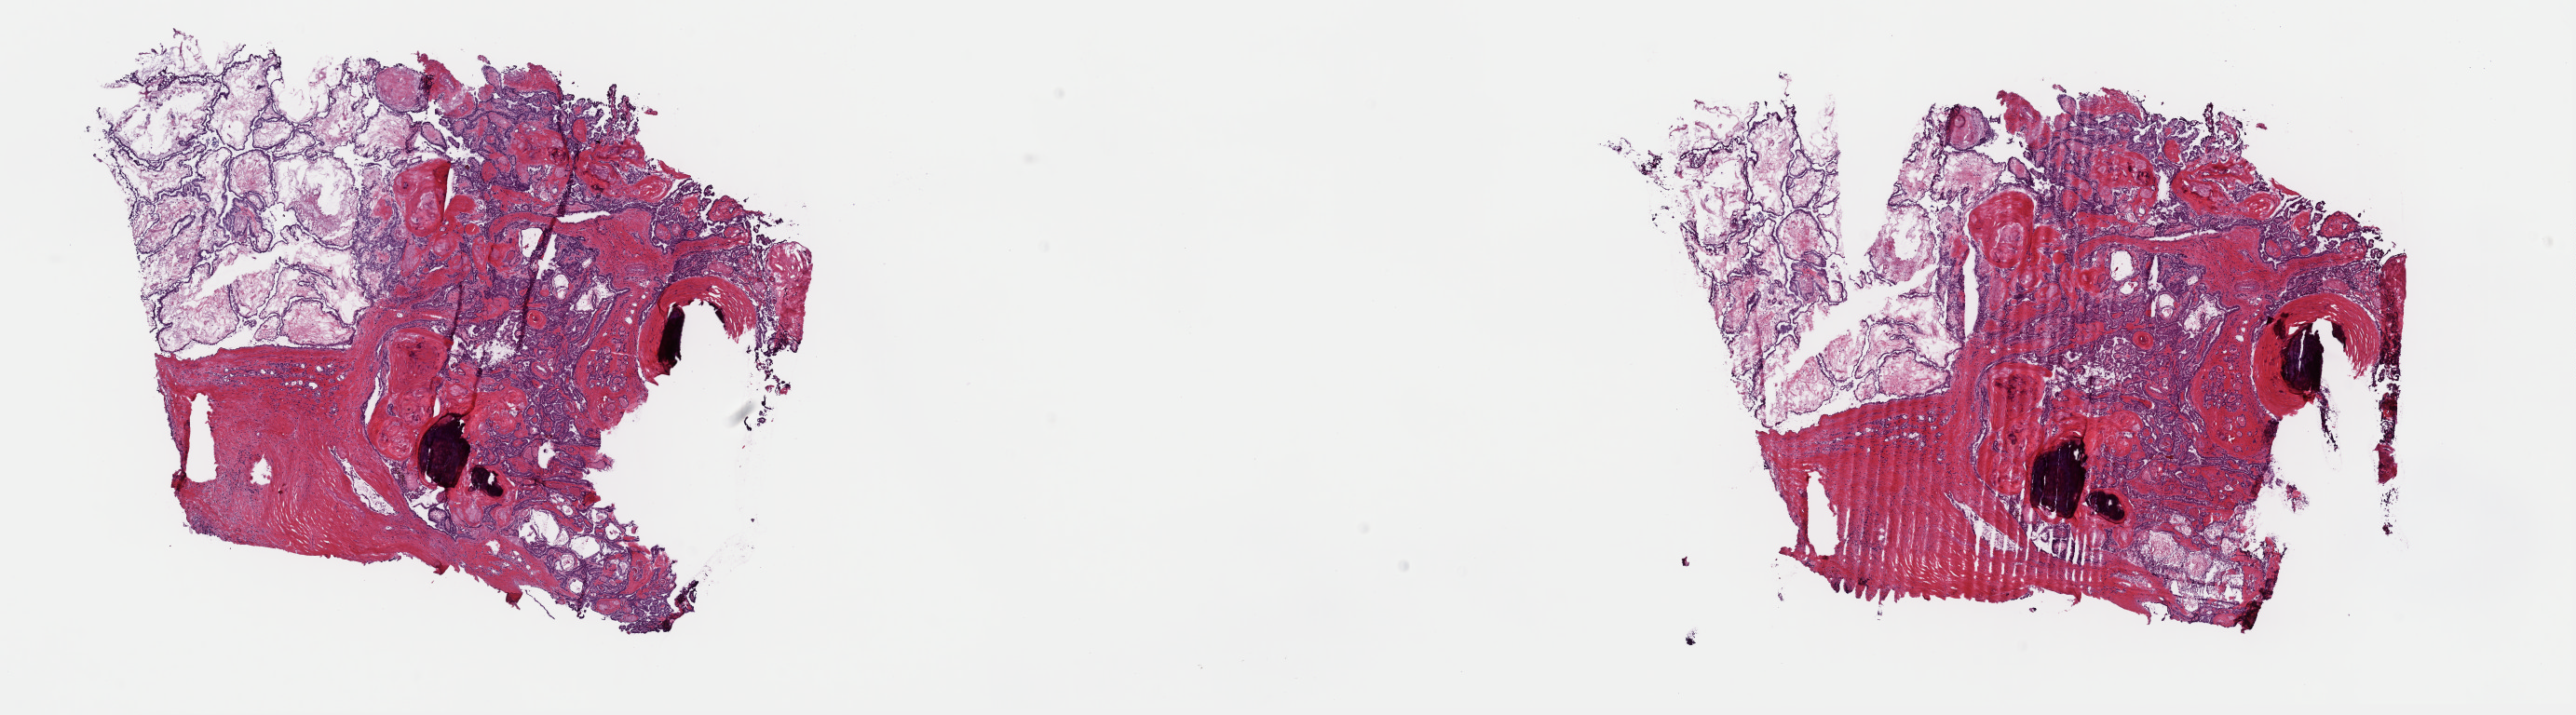
H&E-stained whole-slide image, shown as a low-resolution overview of the whole scanned area (about 21.9 x 6.1 mm); frozen section from the top of the tissue portion; primary tumour sample from the thyroid. Female, age 45 years at initial diagnosis.
Histologic diagnosis: Papillary adenocarcinoma, NOS (thyroid gland).